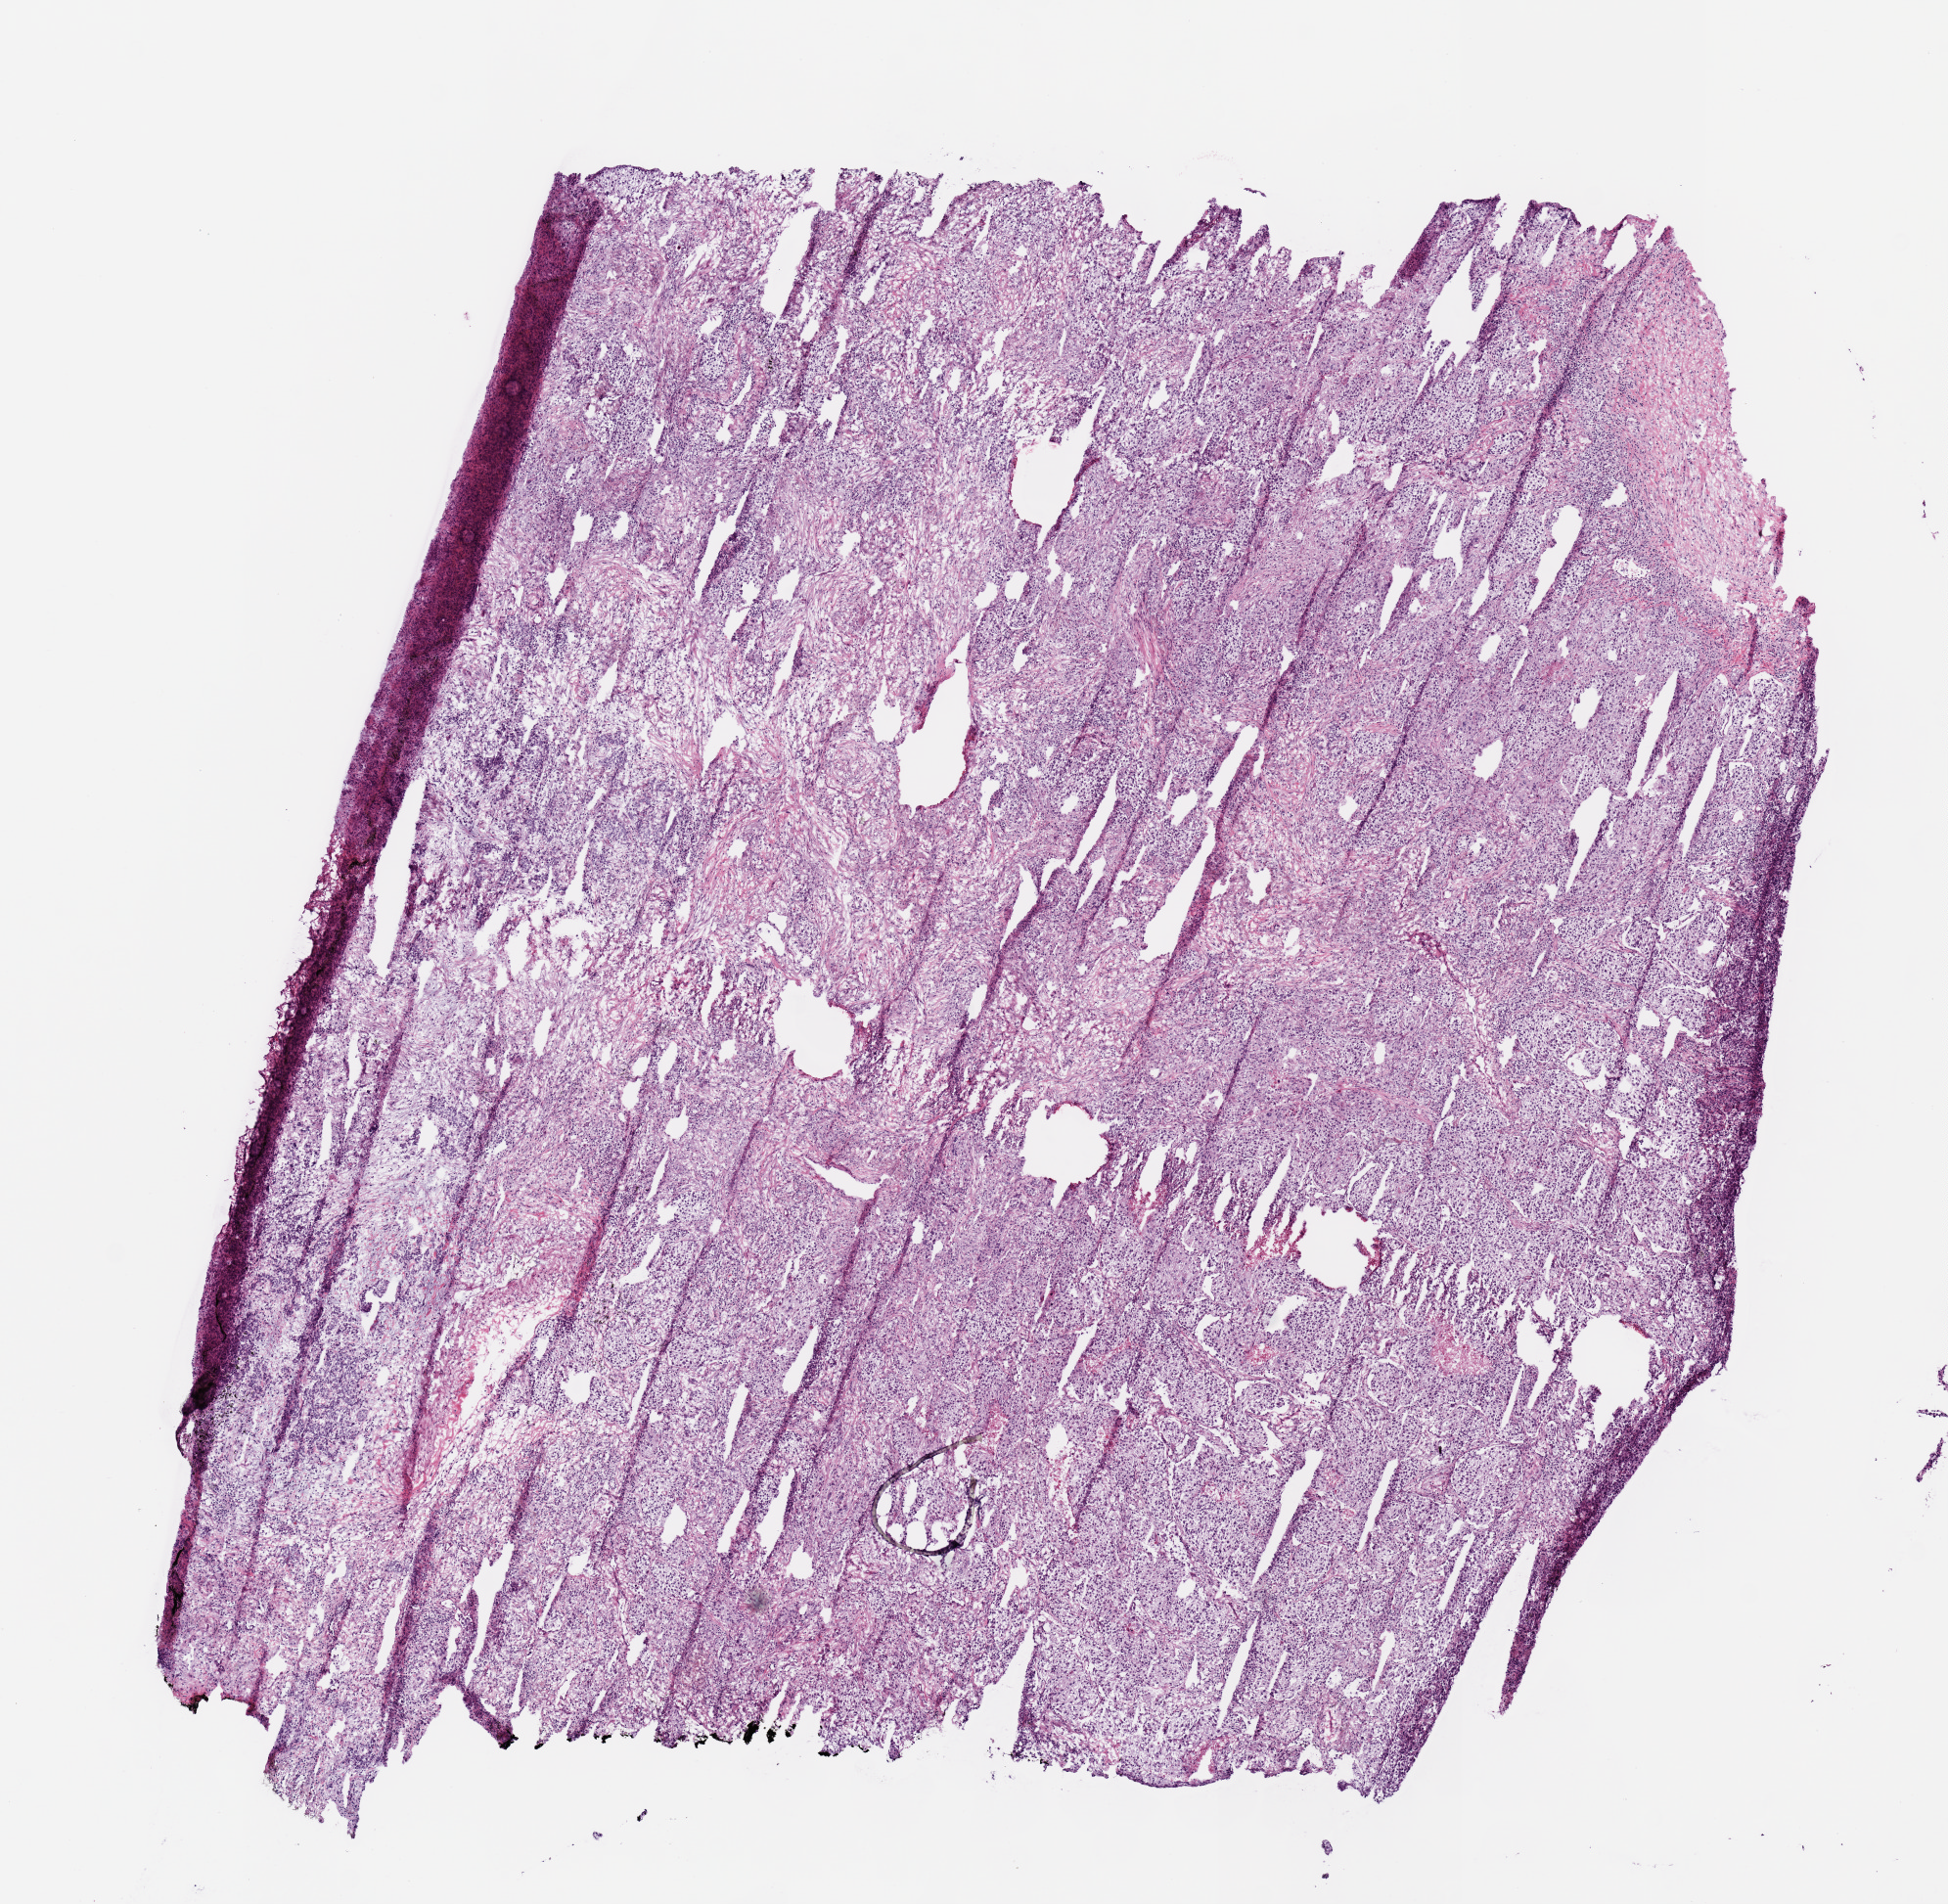
Hematoxylin and eosin (H&E) stained whole-slide image, a low-resolution overview of the entire scanned area, about 7.9 x 7.7 mm (acquisition: 20x scan). Frozen section from the top of the tissue portion. Lung, primary tumour sample. Female patient; age at initial diagnosis 66 years.
Pathologic diagnosis: Squamous cell carcinoma, NOS.